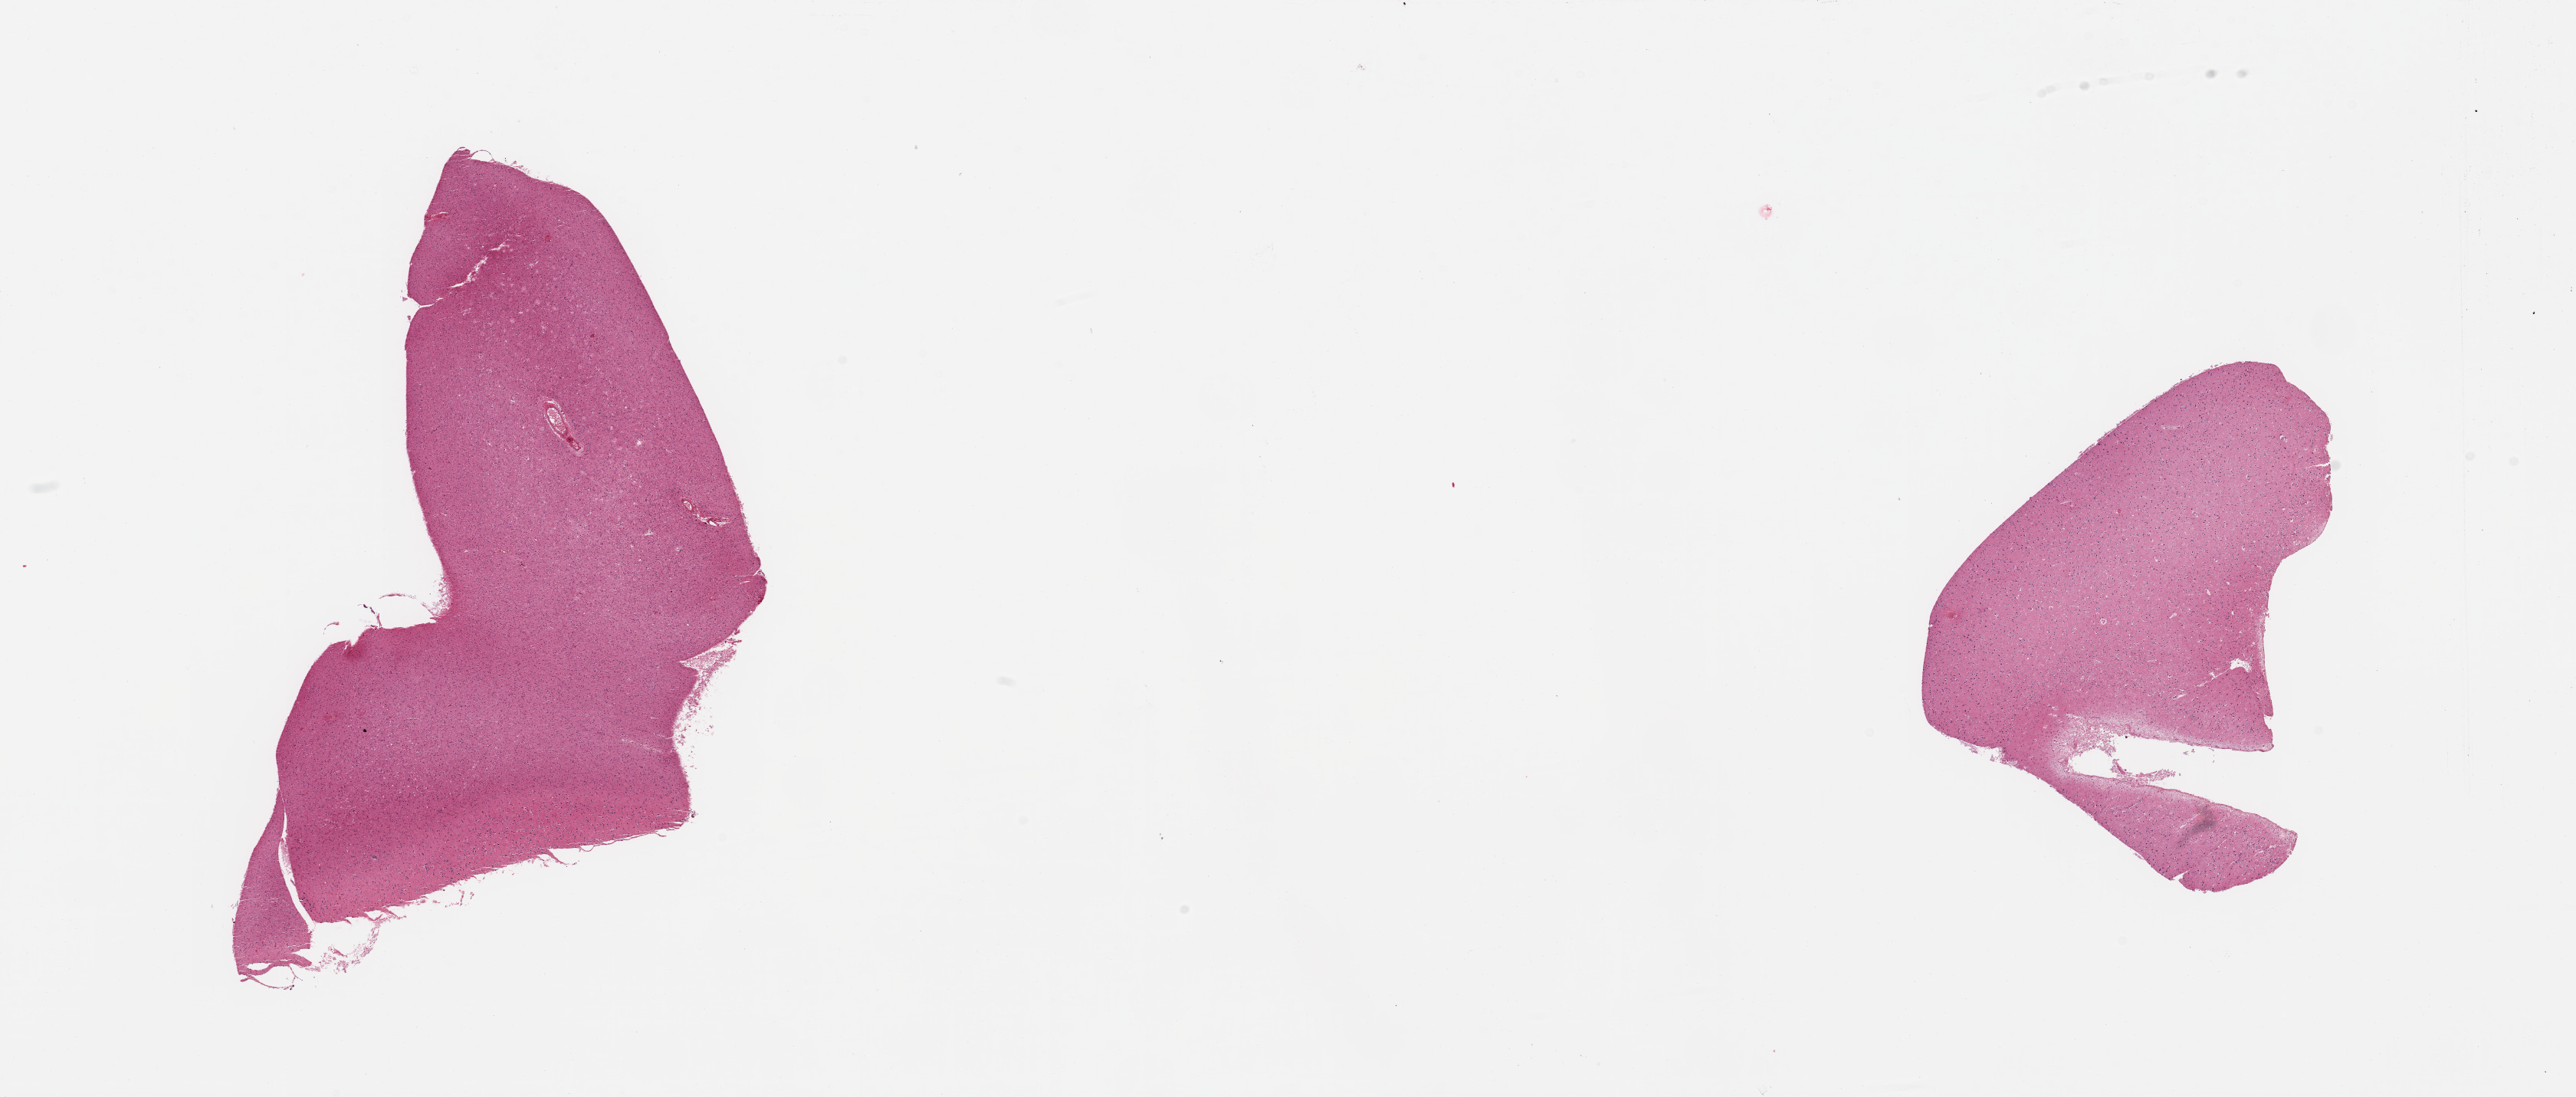
H&E whole-slide image, brightfield — whole scanned area (about 26.6 x 11.3 mm) shown as a low-resolution overview, PAXgene-fixed paraffin-embedded (PFPE) section, section of cerebral cortex (target tissue), tissue donor sample. Donor: male.
- review note (as recorded): 2 pieces, no abnormalities